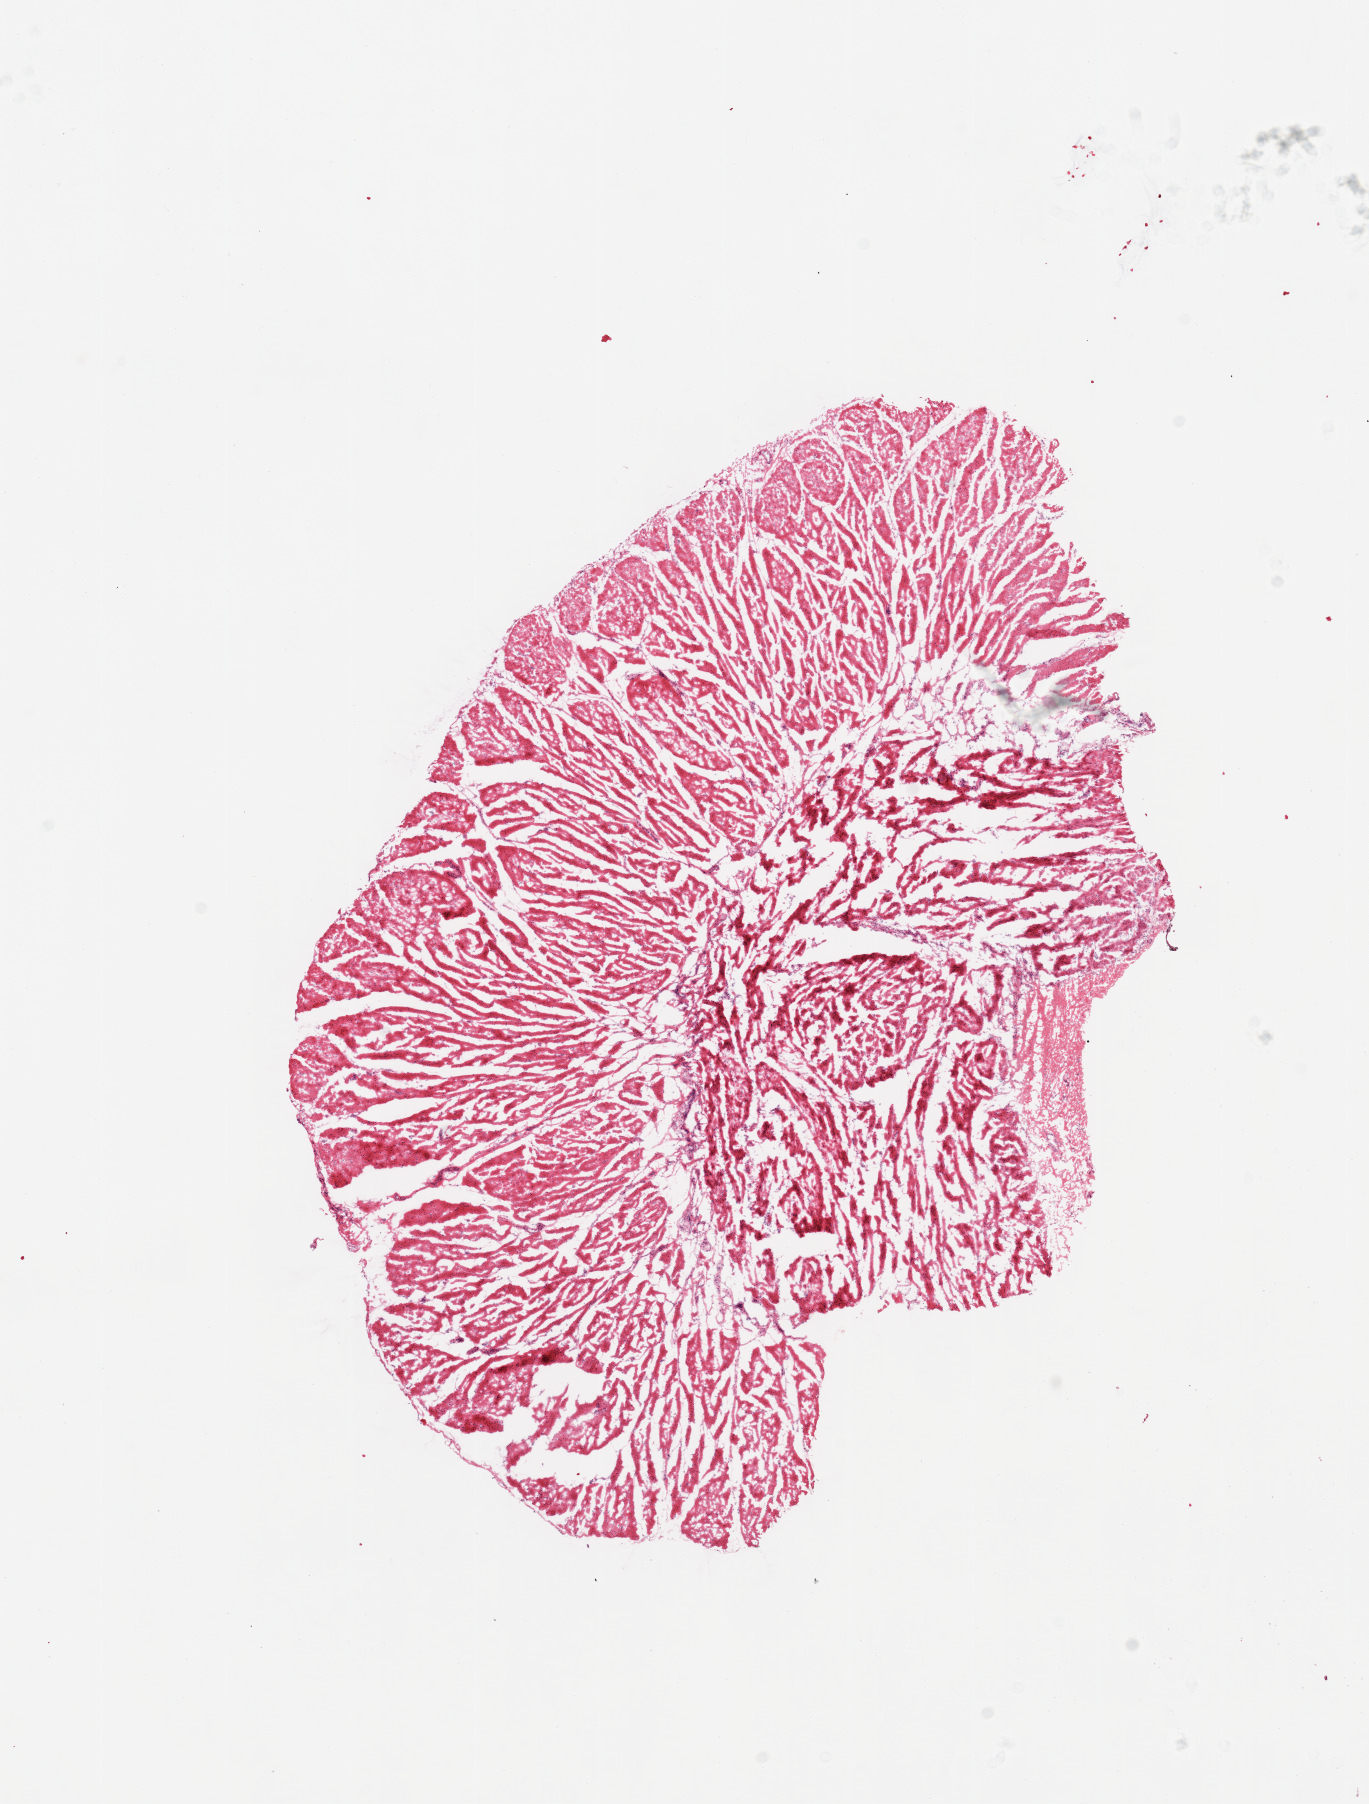
Whole-slide image, hematoxylin and eosin (H&E) stain — a low-resolution overview of the entire scanned area, about 10.8 x 14.3 mm.
Specimen: frozen section; target tissue: esophageal muscle; tissue donor sample.